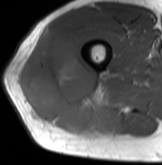
MRI of an extremity soft-tissue mass, one axial slice; slice 46 of 61 in the series (ordered by position); MR volume resampled by the dataset authors to the PET/CT grid (not the native acquisition matrix); 3.27 mm slice thickness; 162 × 165 image matrix, field of view 158 × 161 mm. Male patient. Case-level facts recorded for this patient, not image findings: histological type: poorly differentiated synovial sarcoma; grade: high; site of the primary tumour: right buttock.
Outlined on this slice (expert contour drawn on MRI and transferred to this co-registered scan by the dataset authors):
- gross tumour volume including surrounding oedema: bounding box (x1, y1, x2, y2) in pixels: (22, 31, 110, 133)
- gross tumour volume (mass): (22, 31, 106, 133)